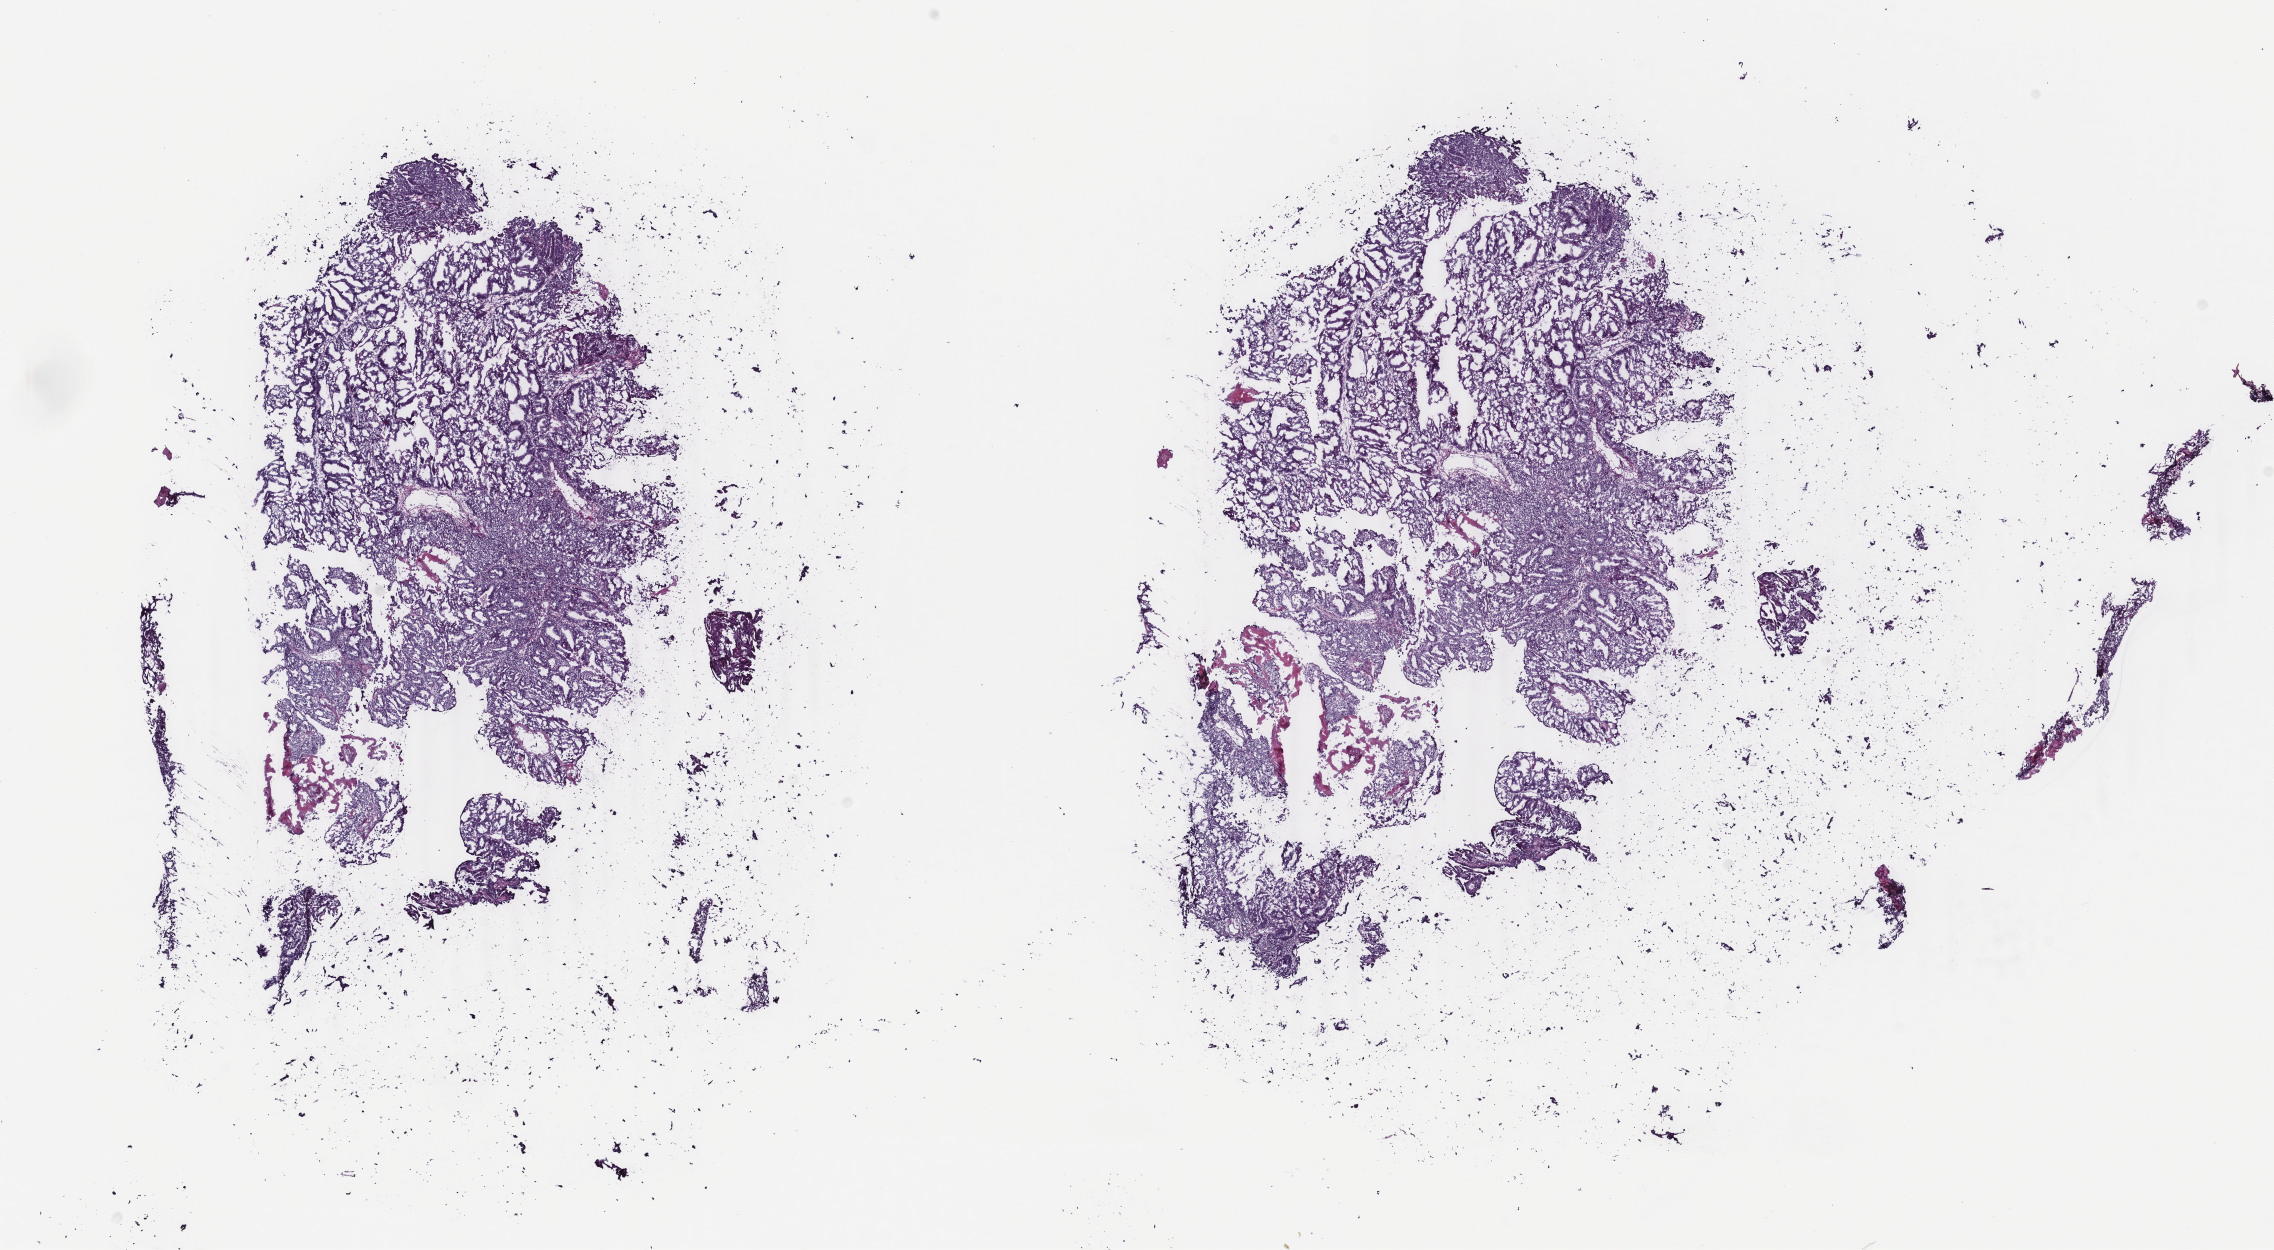
Whole-slide histology image, Hematoxylin and eosin (H&E) stained, whole scanned area (about 18.1 x 9.9 mm) shown as a low-resolution overview. Frozen section. Uterus, primary tumour sample. Female, age 64 years at initial diagnosis. Histologic grade: G2 (moderately differentiated). Pathologist review of this section (percent, as recorded): tumour cells 92%, tumour nuclei 92%, normal cells 0%, stromal cells 7%, necrosis 1%. Infiltration values recorded for this section: lymphocyte infiltration 8%, monocyte infiltration 10%, neutrophil infiltration 1%.
- diagnosis: Endometrioid adenocarcinoma, NOS (endometrium)
- FIGO stage: IA
- lymph nodes positive (case pathology): 0 of 17 examined